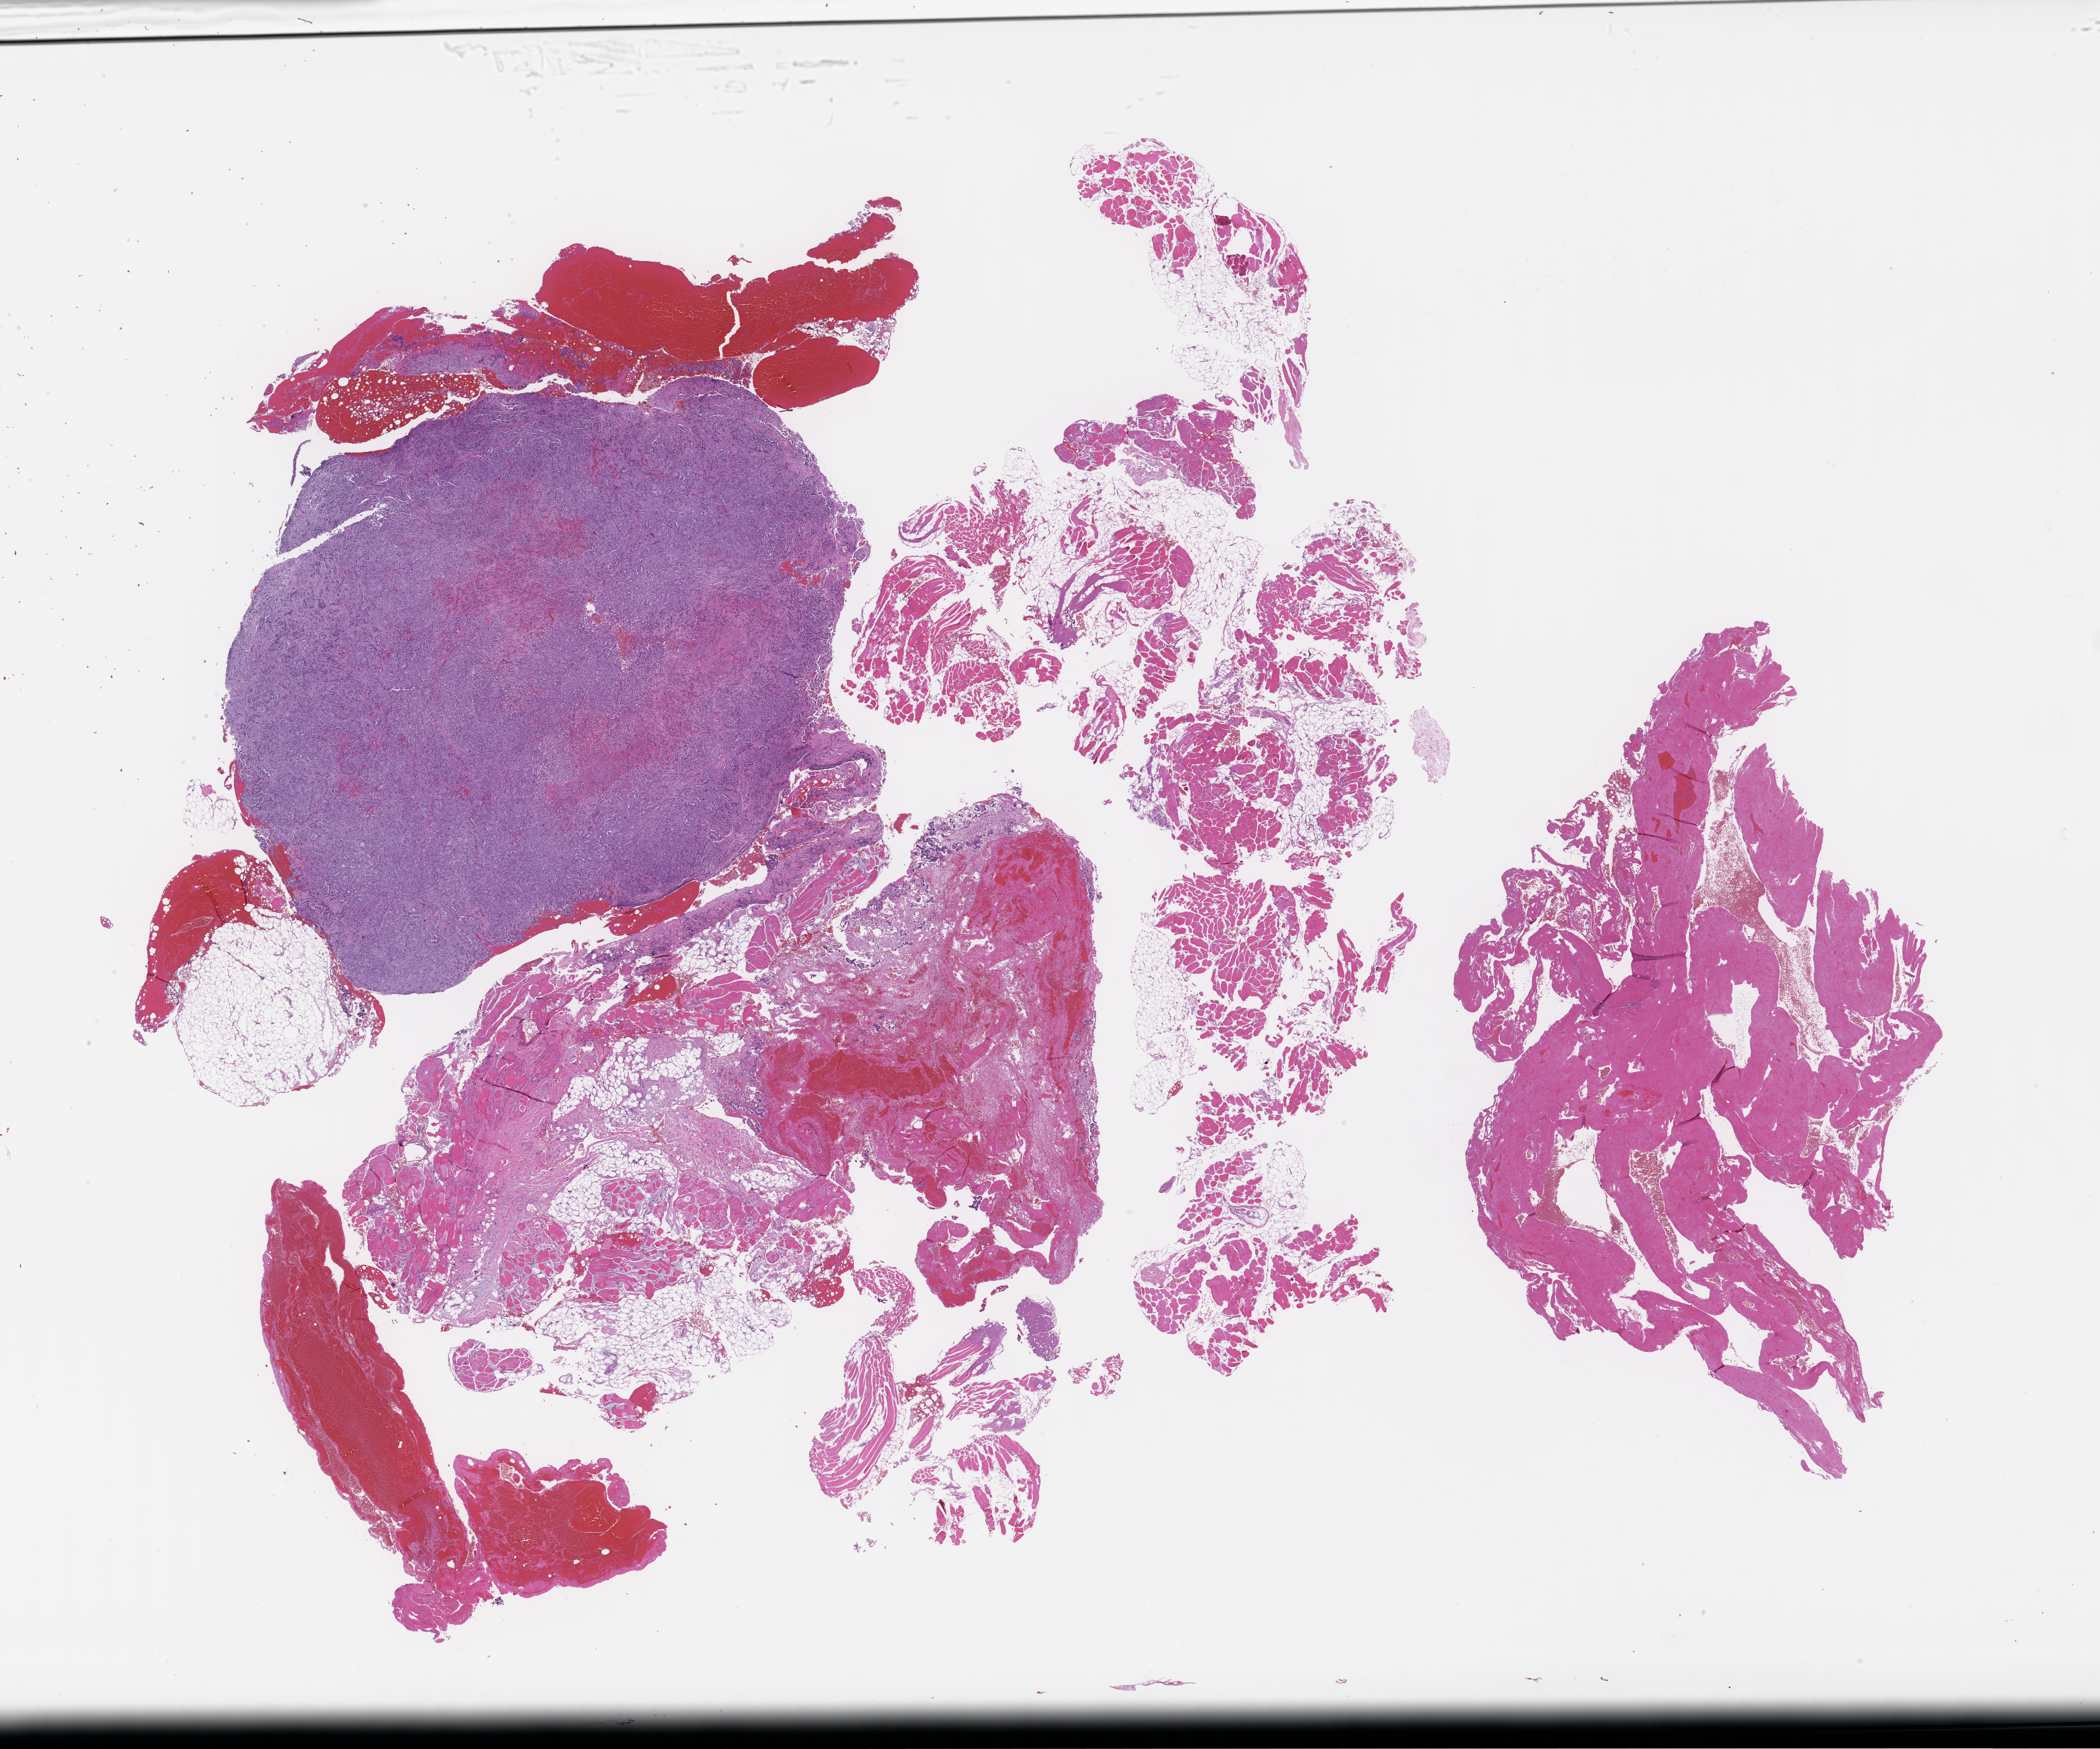
Whole-slide image, hematoxylin and eosin (H&E) stain — whole scanned area (about 29.1 x 24.3 mm) shown as a low-resolution overview, formalin-fixed paraffin-embedded section, archival tissue. Patient sex: male.
• this section: metastatic tumor tissue
• primary diagnosis of the patient: Non-Small Cell Lung Carcinoma